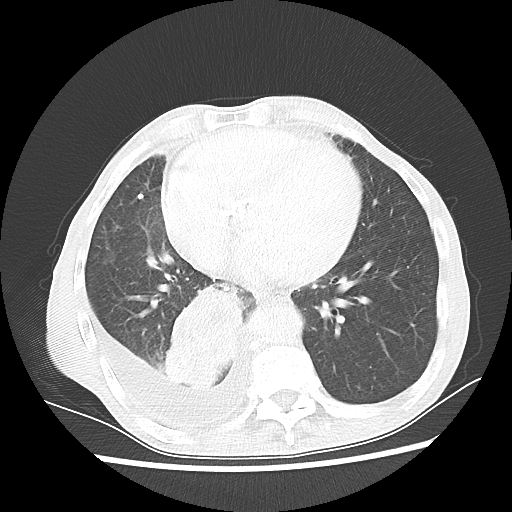
Chest CT, one axial slice. Position 23 of 60 along the scan axis. Reconstruction kernel LUNG. Lung window (W 1500 / L -600 HU). 512 × 512 image matrix, field of view 335 × 335 mm. Patient: male, 76 years. Case-level facts recorded for this patient, not image findings: clinical TNM (as recorded): T3 N3 M1a; histopathological grade: G3.
Structures marked on this image (rectangle marked by the reading radiologist):
- lung tumour (recorded histology: squamous cell carcinoma): box from (x=160, y=281) to (x=247, y=393) px